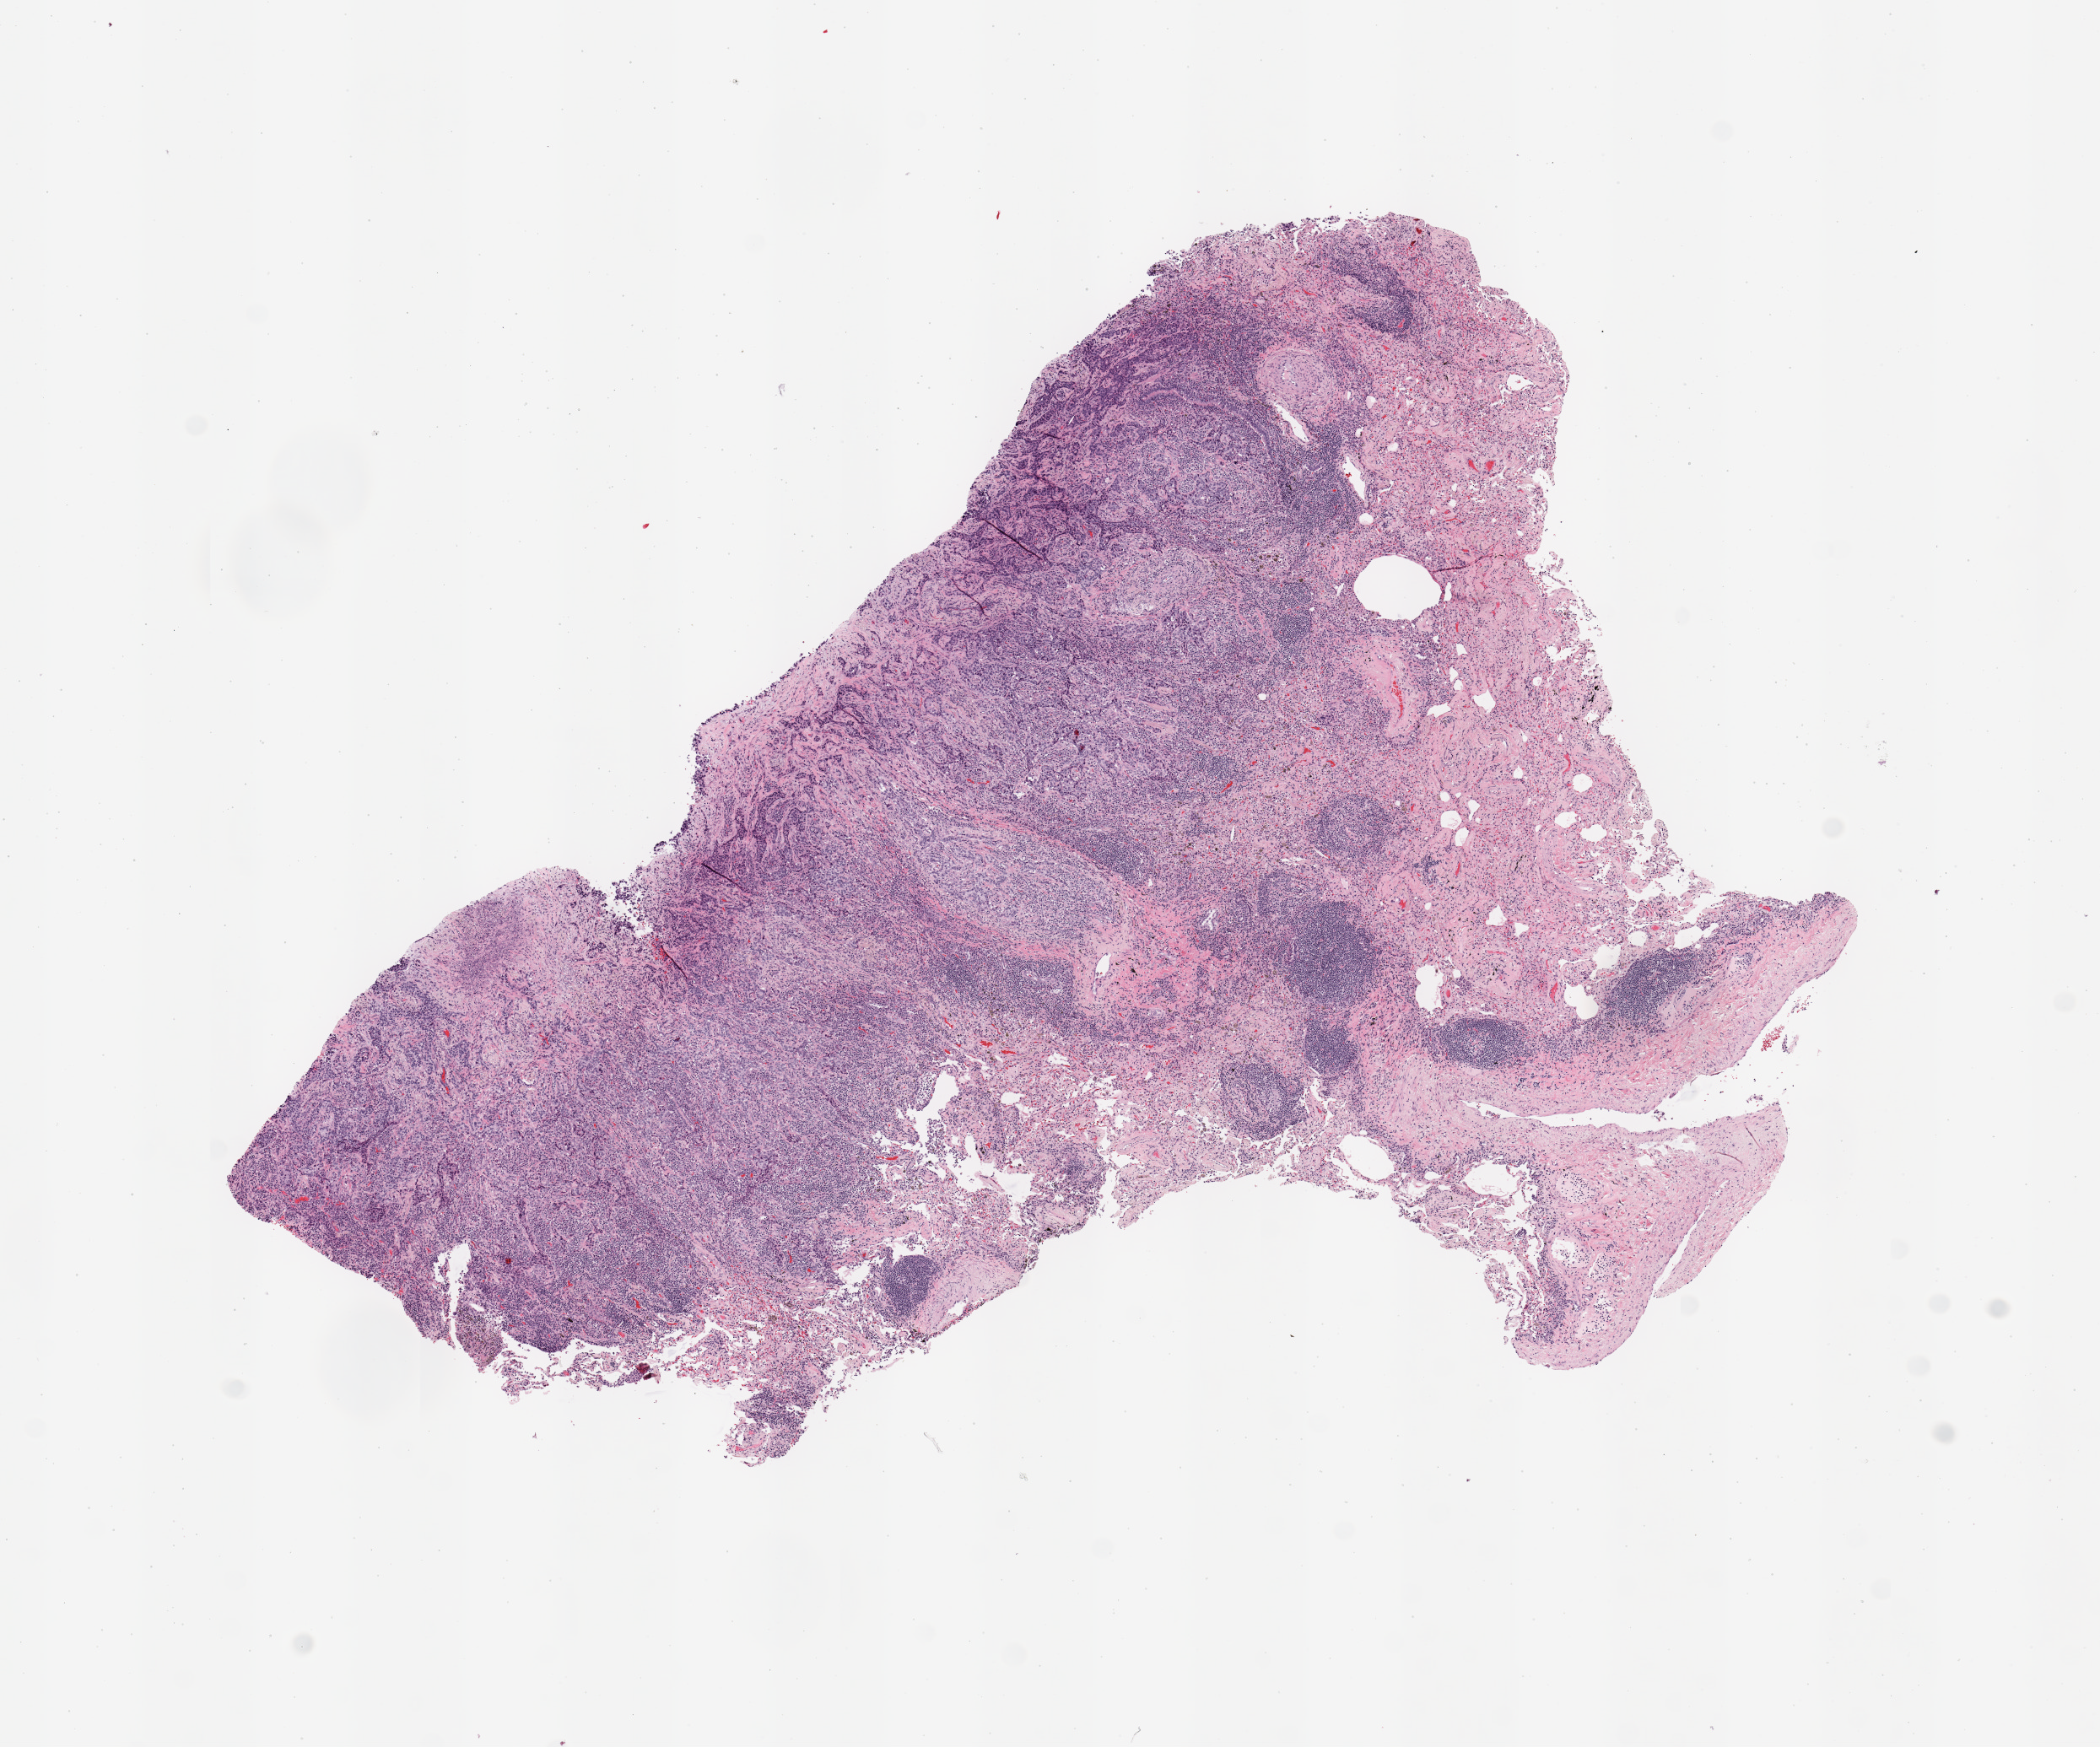
Whole-slide histology image, H&E-stained — a low-resolution overview of the entire scanned area, about 9.8 x 8.2 mm; tumour tissue sample, sampled site: lung. Male, 58 y/o. Histologic grade: G2 (moderately differentiated). Pathologist review of this section (percent, as recorded): tumour nuclei 70%, necrosis 0%.
AJCC pathologic stage: IB. Primary tumour site (as recorded): left lower lobe. Diagnosis: Adenocarcinoma, NOS.